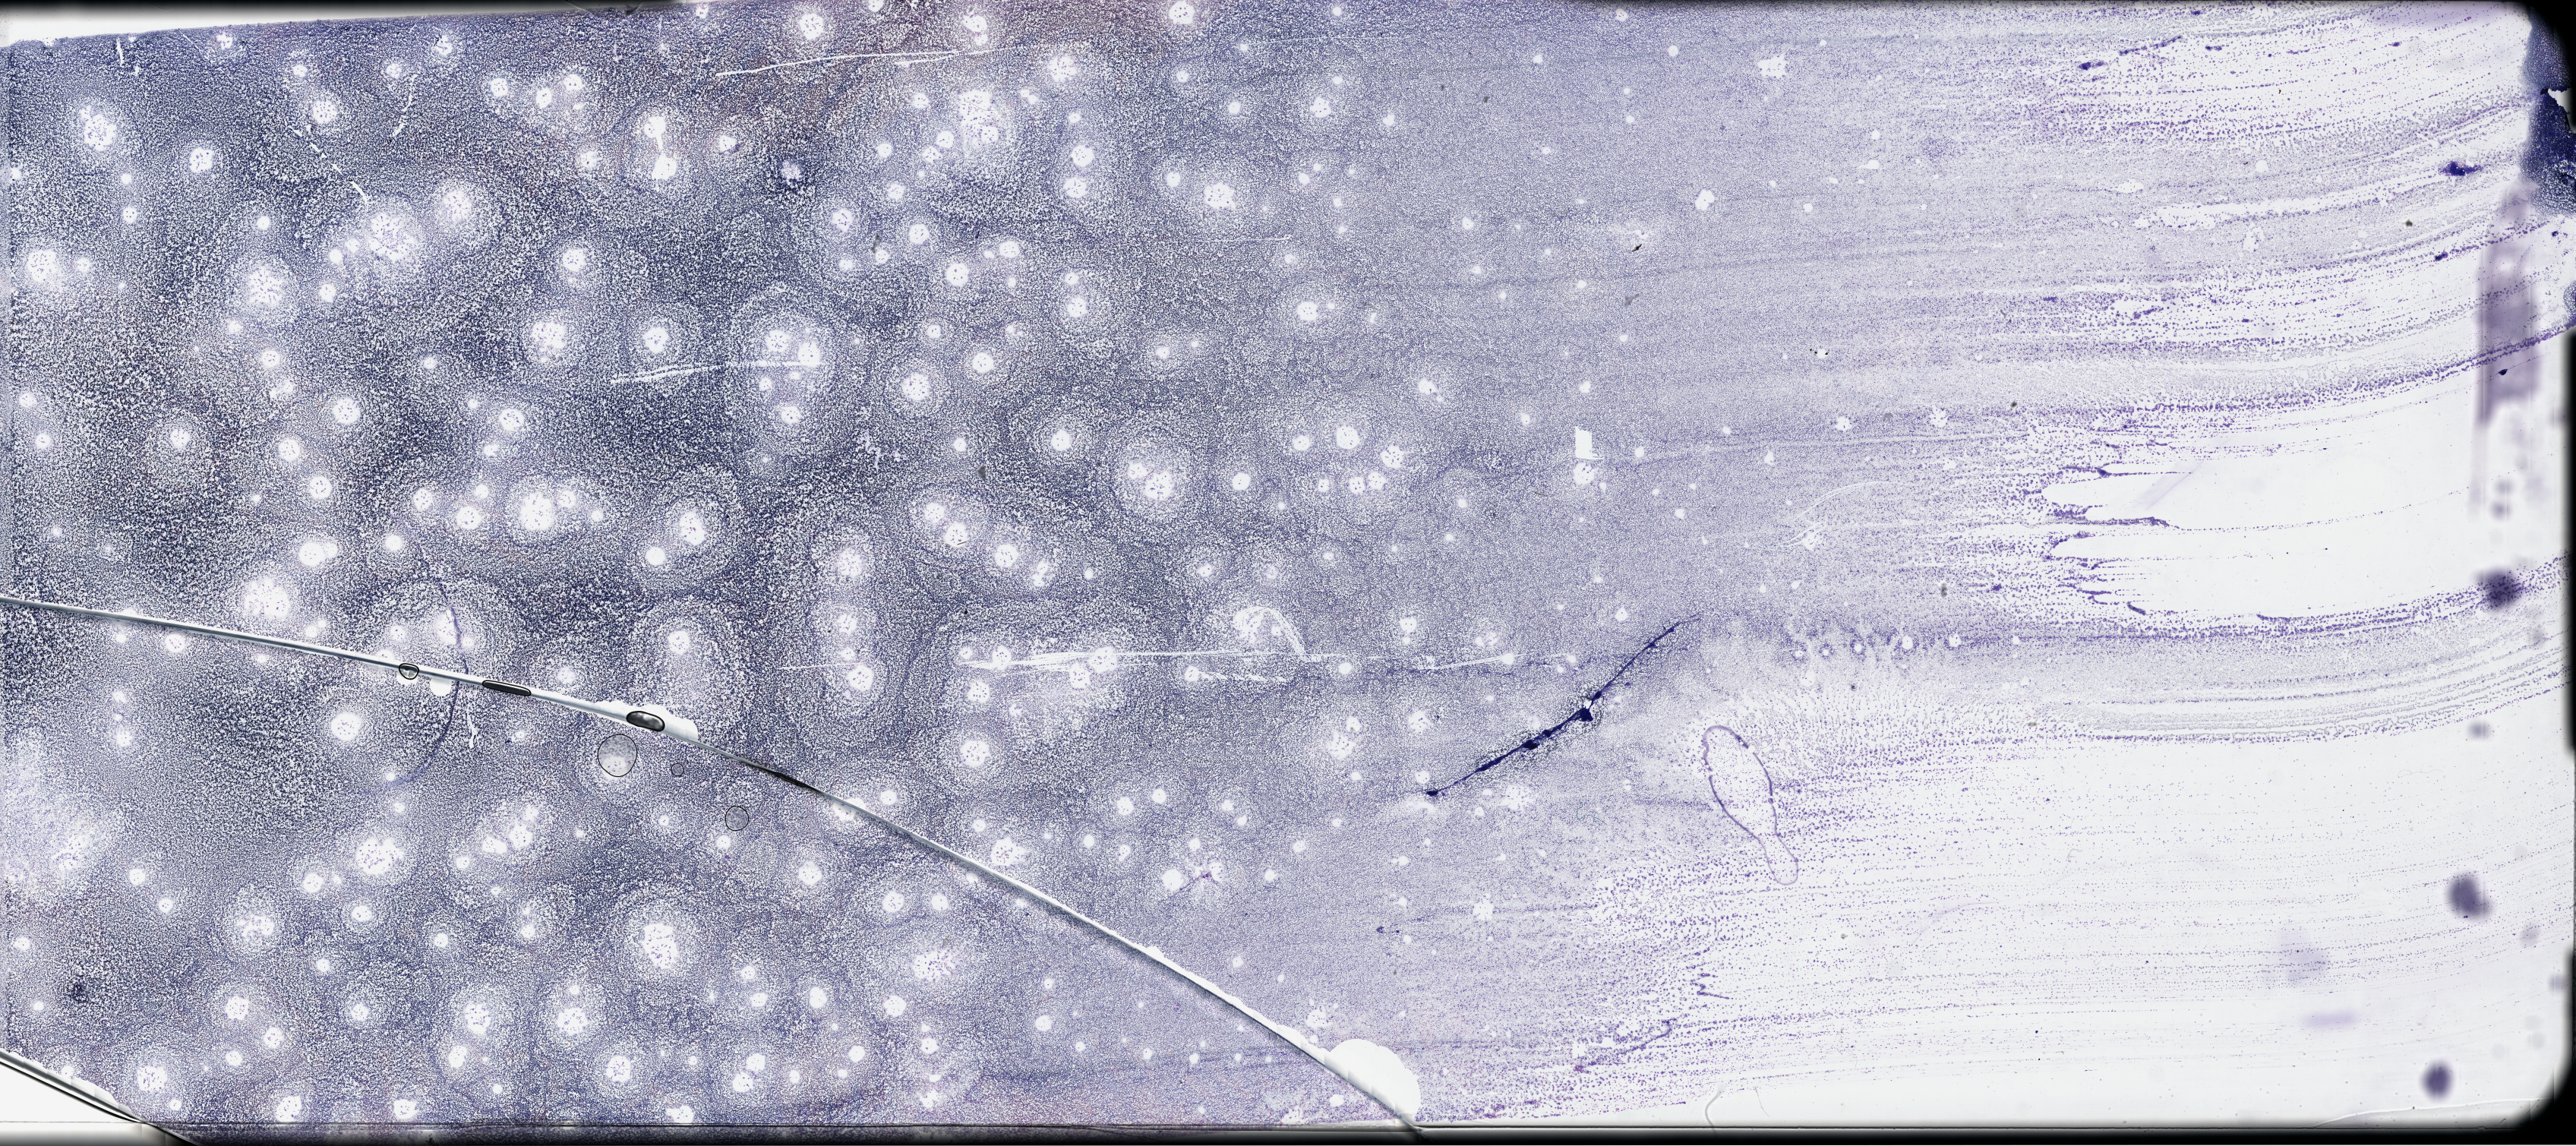
Whole-slide histology image, Hematoxylin and eosin (H&E) stained, a low-resolution overview of the entire scanned area, about 54.8 x 24.4 mm, peripheral blood (leukaemic) sample. Female, 60 y/o.
WHO classification: Acute monoblastic and monocytic leukemia. Diagnosis: Acute Myeloid Leukemia. FAB classification: M5.